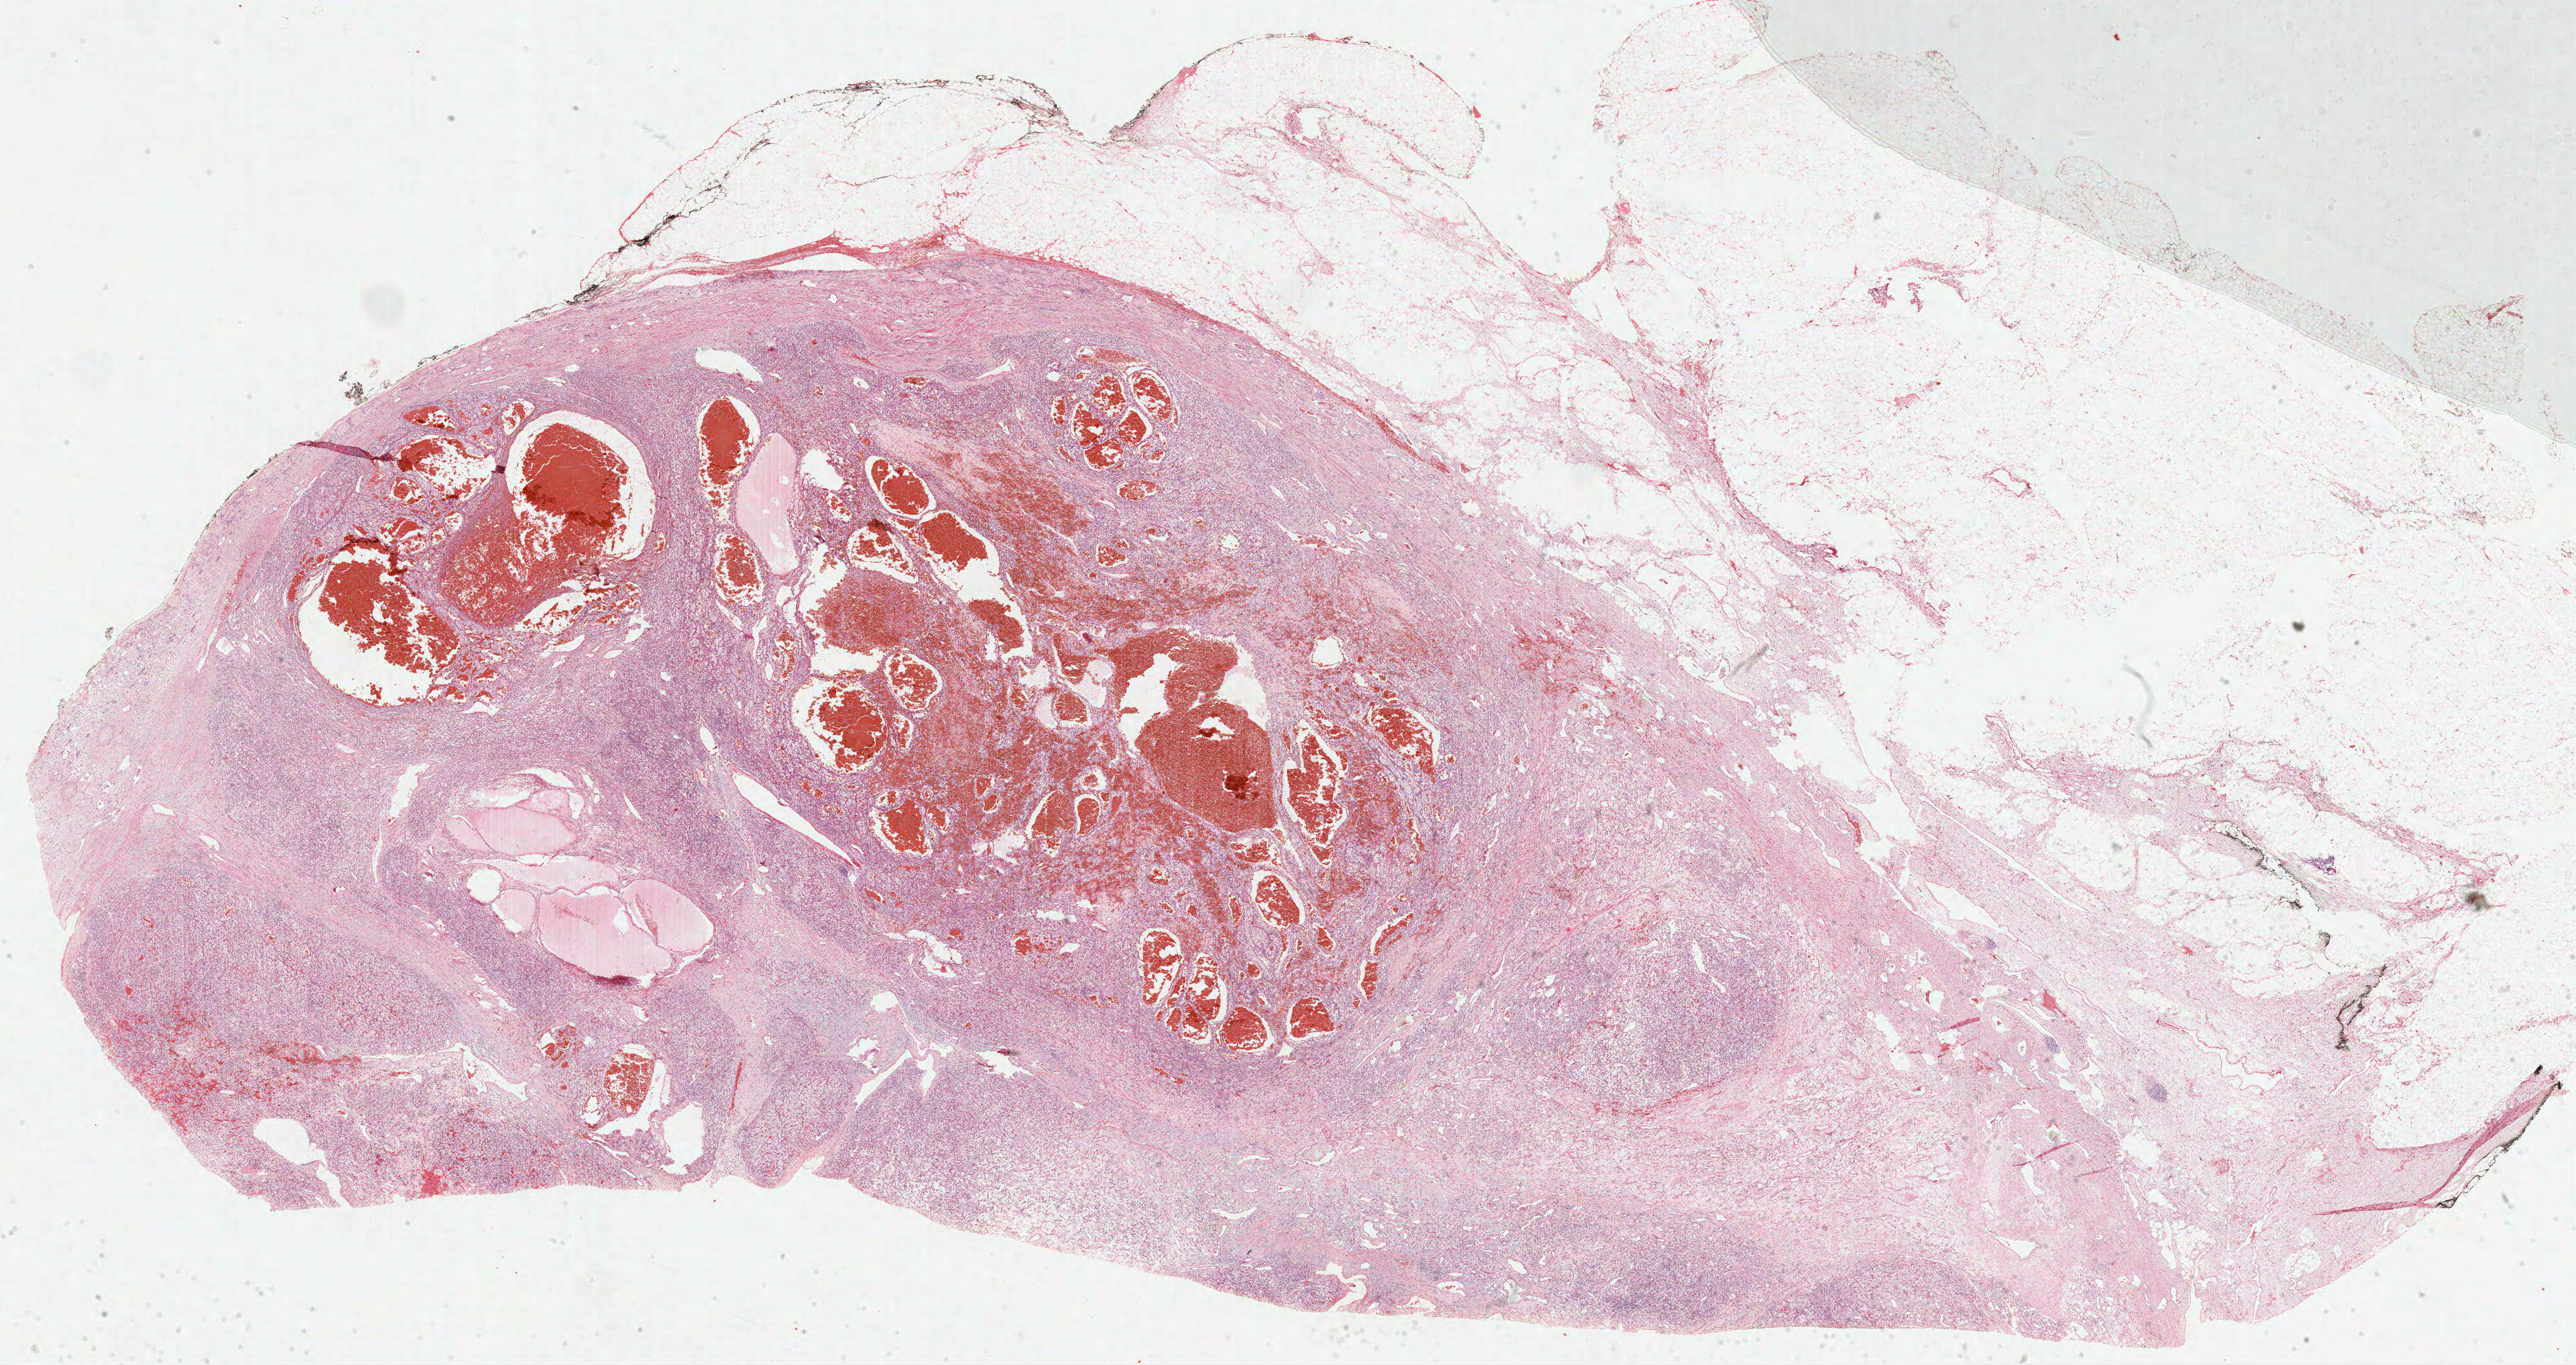
Digitized H&E tissue section (whole slide), shown as a low-resolution overview of the whole scanned area (about 30.2 x 16.0 mm, acquisition: 40x scan); formalin-fixed paraffin-embedded (FFPE) diagnostic section; sample: primary tumour, kidney. Female patient; age at initial diagnosis 74 years.
Pathologic diagnosis: Clear cell adenocarcinoma, NOS.